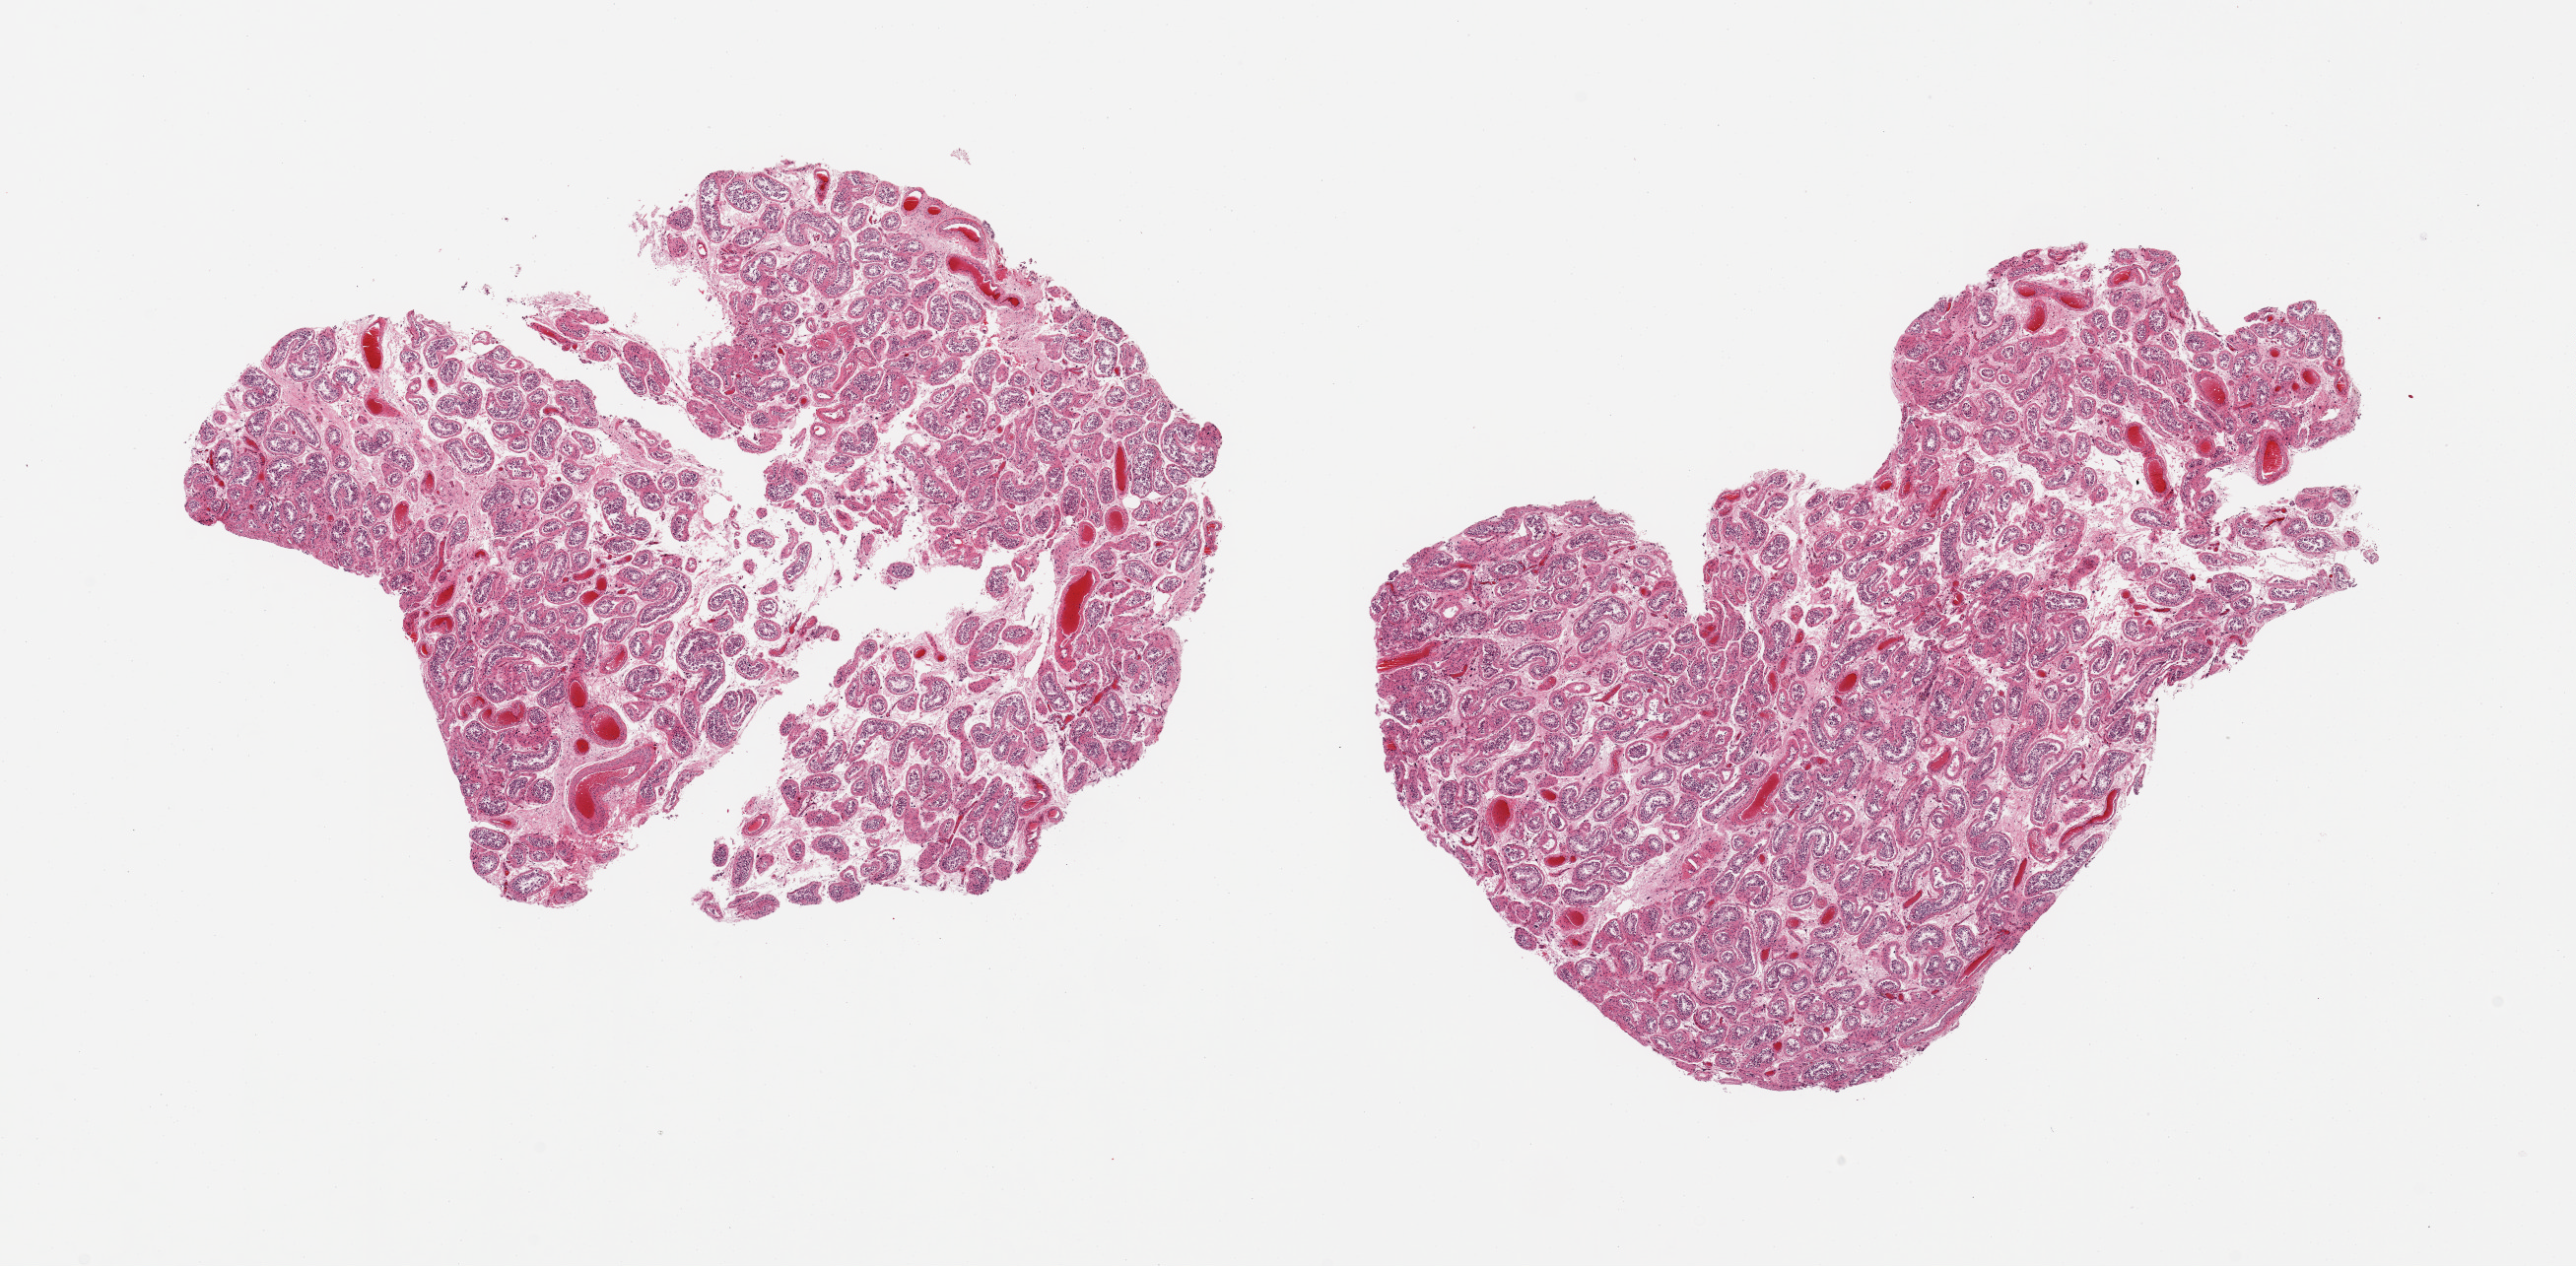
Digitized hematoxylin and eosin (H&E)-stained section — whole scanned area (about 20.7 x 10.2 mm) shown as a low-resolution overview. PAXgene-fixed, paraffin-embedded tissue. Sampled site (target tissue): testis. Tissue donor sample. Donor sex: male.
* reviewer comment on this tissue sample: 2 pieces; decreased sperm maturation